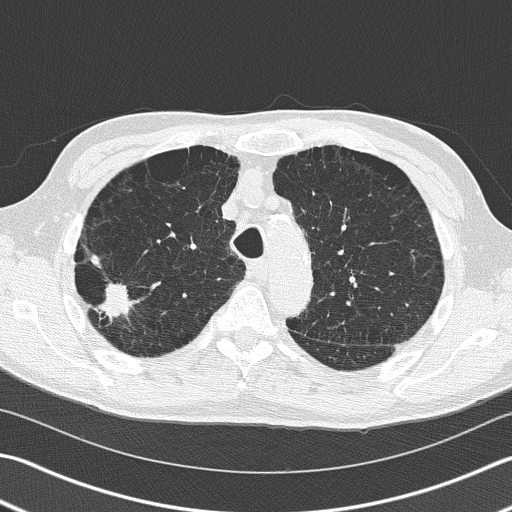
Low-dose screening chest CT, one axial slice. Slice 118 of 163 in the series (ordered by position). Reconstruction kernel B50f. Lung window (W 1500 / L -600 HU). 2 mm slice thickness. 512 × 512 image matrix.
Structures marked on this image (manually delineated by an expert):
- lesion 1 (tumor, upper lobe of right lung): bounding box [x1, y1, x2, y2] px = [92, 257, 133, 320]